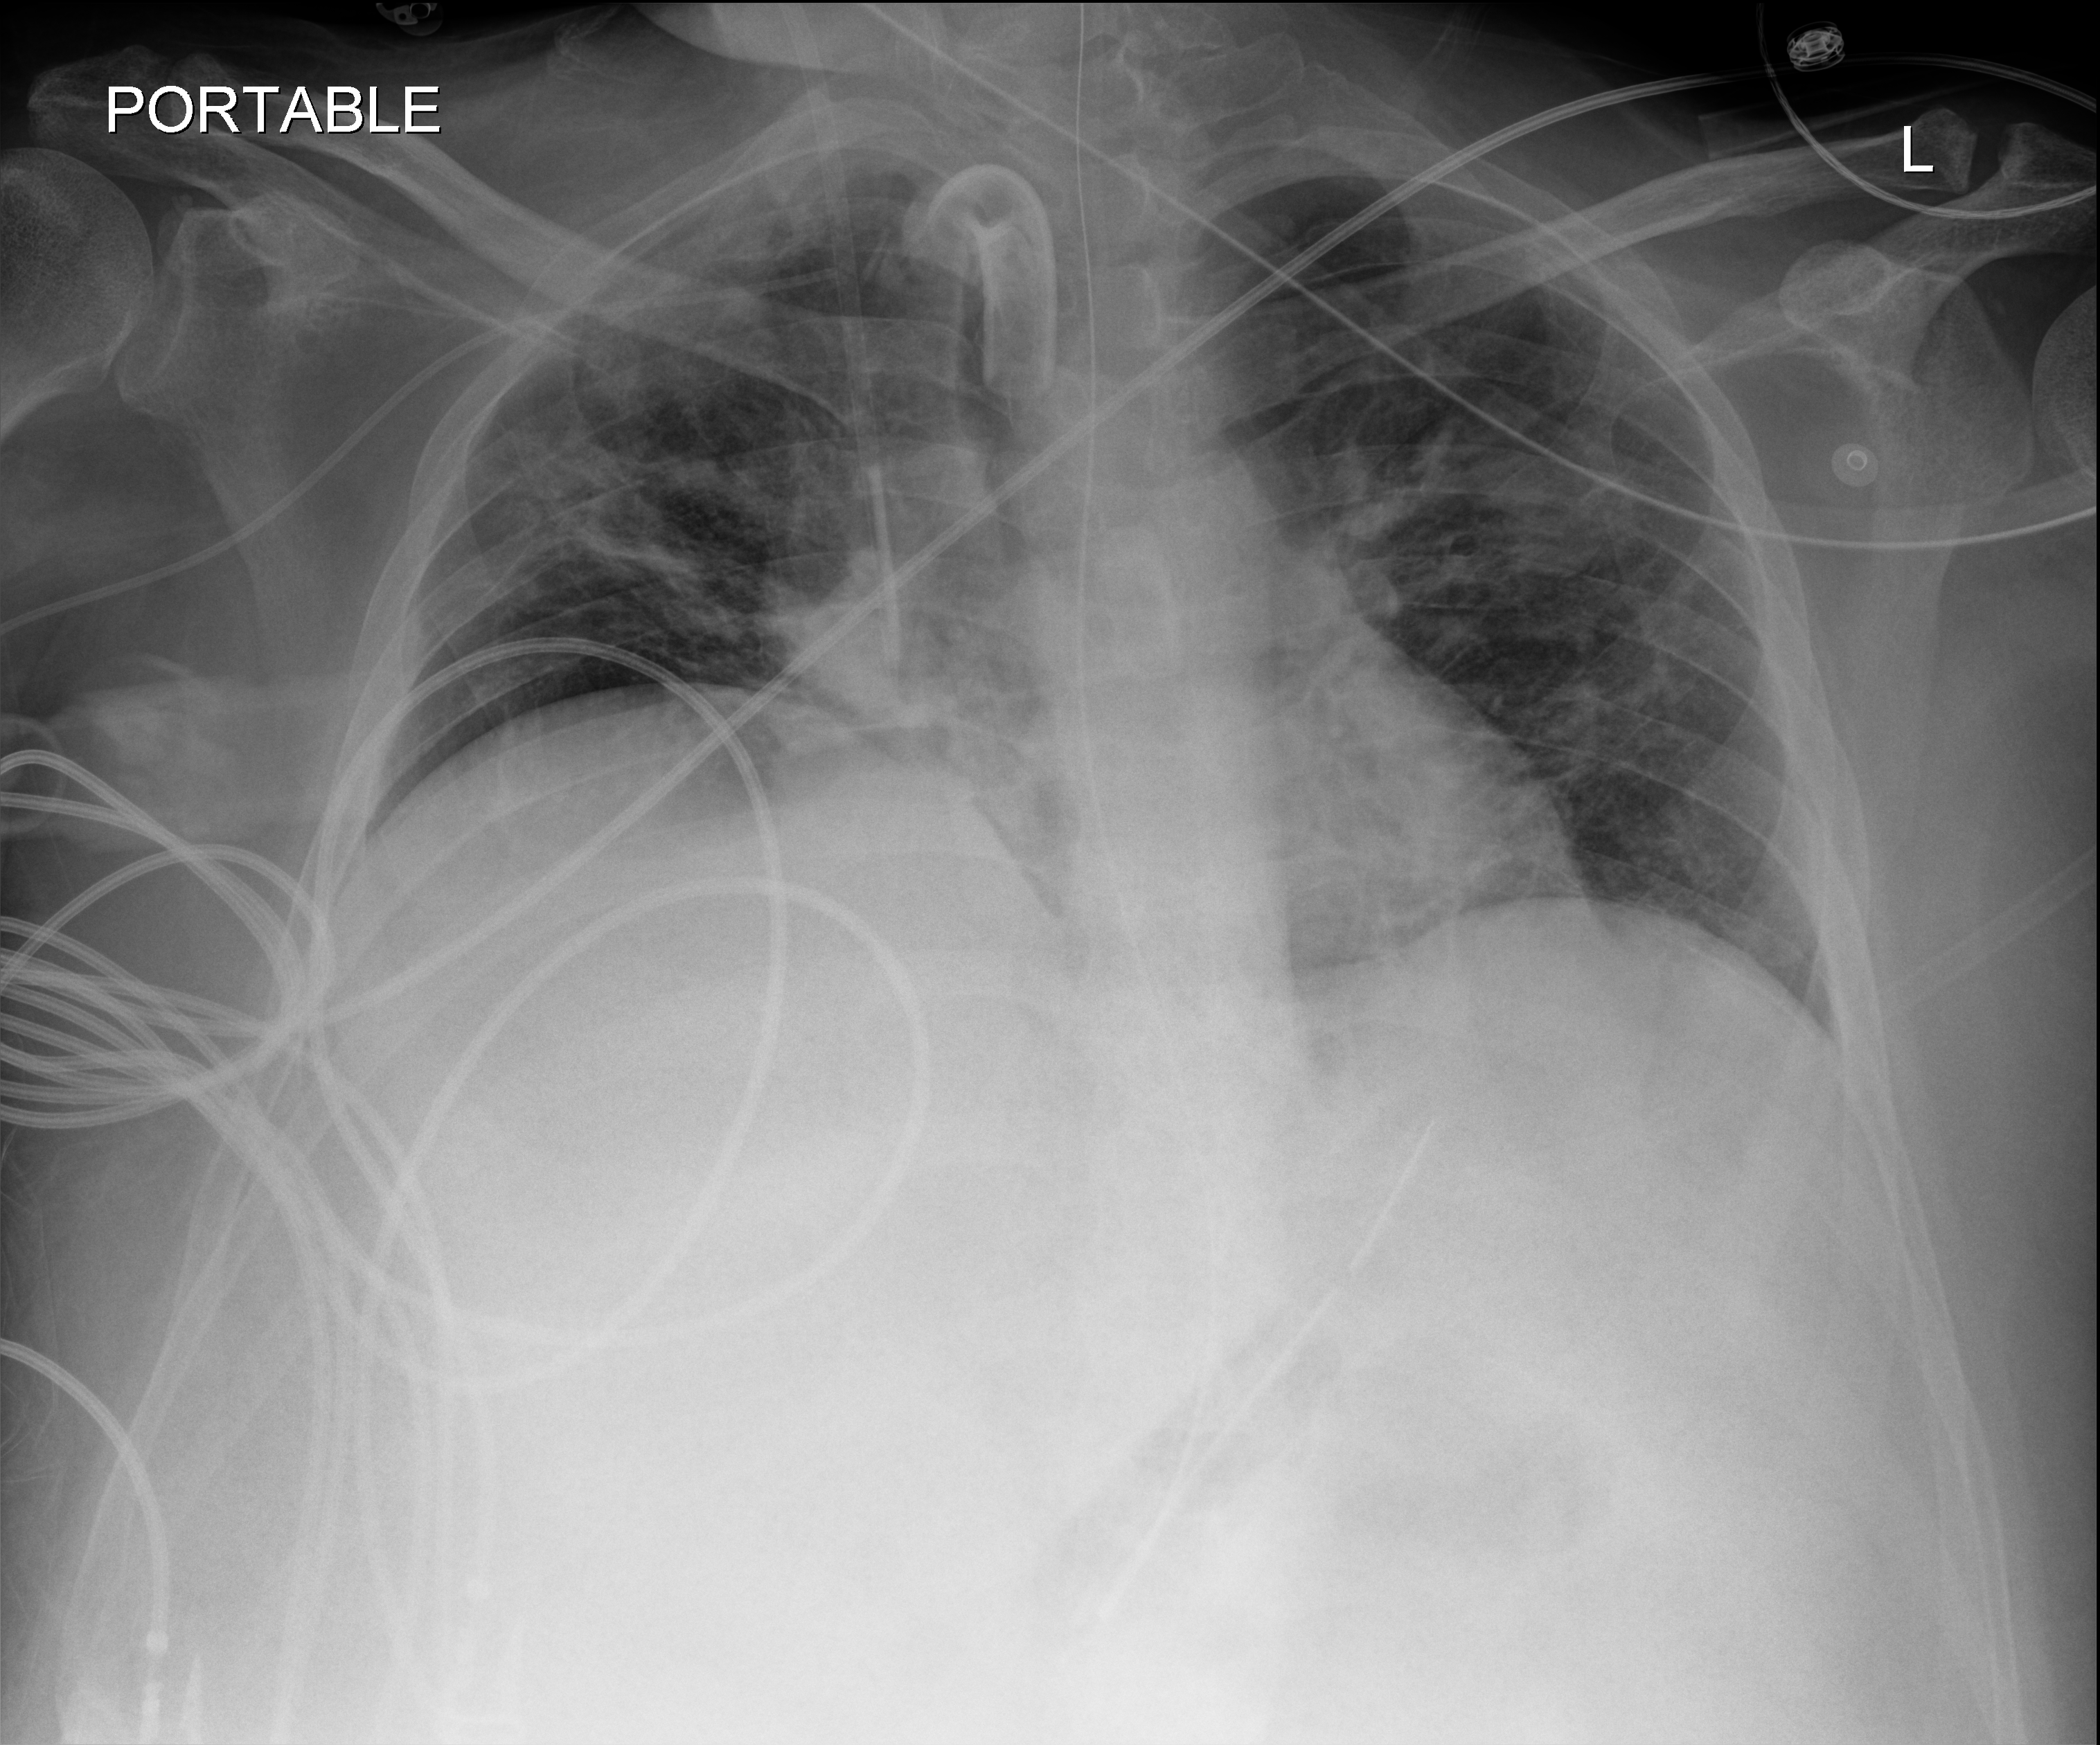
Portable chest radiograph; anteroposterior (AP) projection. Adult patient hospitalised with COVID-19, age 18–59 years.
Admission-level facts for this patient (not findings on this image; timing relative to this image not recorded): hypertension (admission record): yes; admitted to intensive care during this hospital stay: yes; length of hospital stay: 50 days.